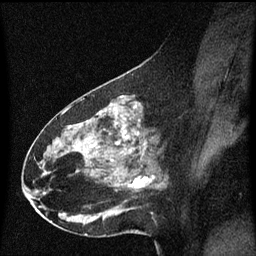
Breast MRI (dynamic contrast-enhanced), one sagittal slice; position 31 of 60 along the scan axis; dynamic contrast-enhanced series, image 2 of 3 at this slice position (ordered by acquisition); 1.5 T; TE 4.2 ms, TR 8.4 ms; 2 mm slice thickness; 256 × 256 image matrix. Female patient, age 49 years. Case-level facts recorded for this patient, not image findings: setting: breast cancer imaged before/during neoadjuvant chemotherapy; receptor status: HR-positive, HER2-negative.
Outlined on this slice (semi-automatically segmented with operator editing):
- analysis volume of interest (the breast-tissue region the enhancement analysis was run in; not a lesion): bounding box <27,96,168,221> (left, top, right, bottom; pixels)
- tumour enhancement mask (voxels above the 70 % enhancement threshold inside the analysis volume of interest): <126,134,146,181>